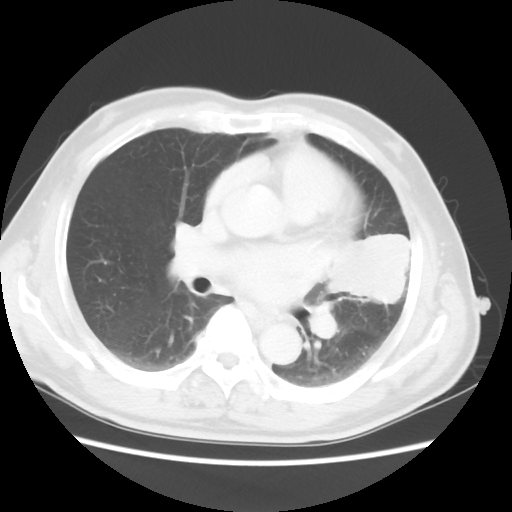
Chest CT, one axial slice. Slice 26 of 50 in the series (ordered by position). 120 kVp. Lung window (W 1500 / L -600 HU). 5 mm slice thickness. 512 × 512 image matrix. Male patient, age 69 years. From the clinical record (not read from this slice): clinical TNM (as recorded): T3 N1 M1a.
Annotated regions visible in this slice (rectangle marked by the reading radiologist):
- lung tumour (recorded histology: squamous cell carcinoma): bounding box <319,218,419,318> (left, top, right, bottom; pixels)